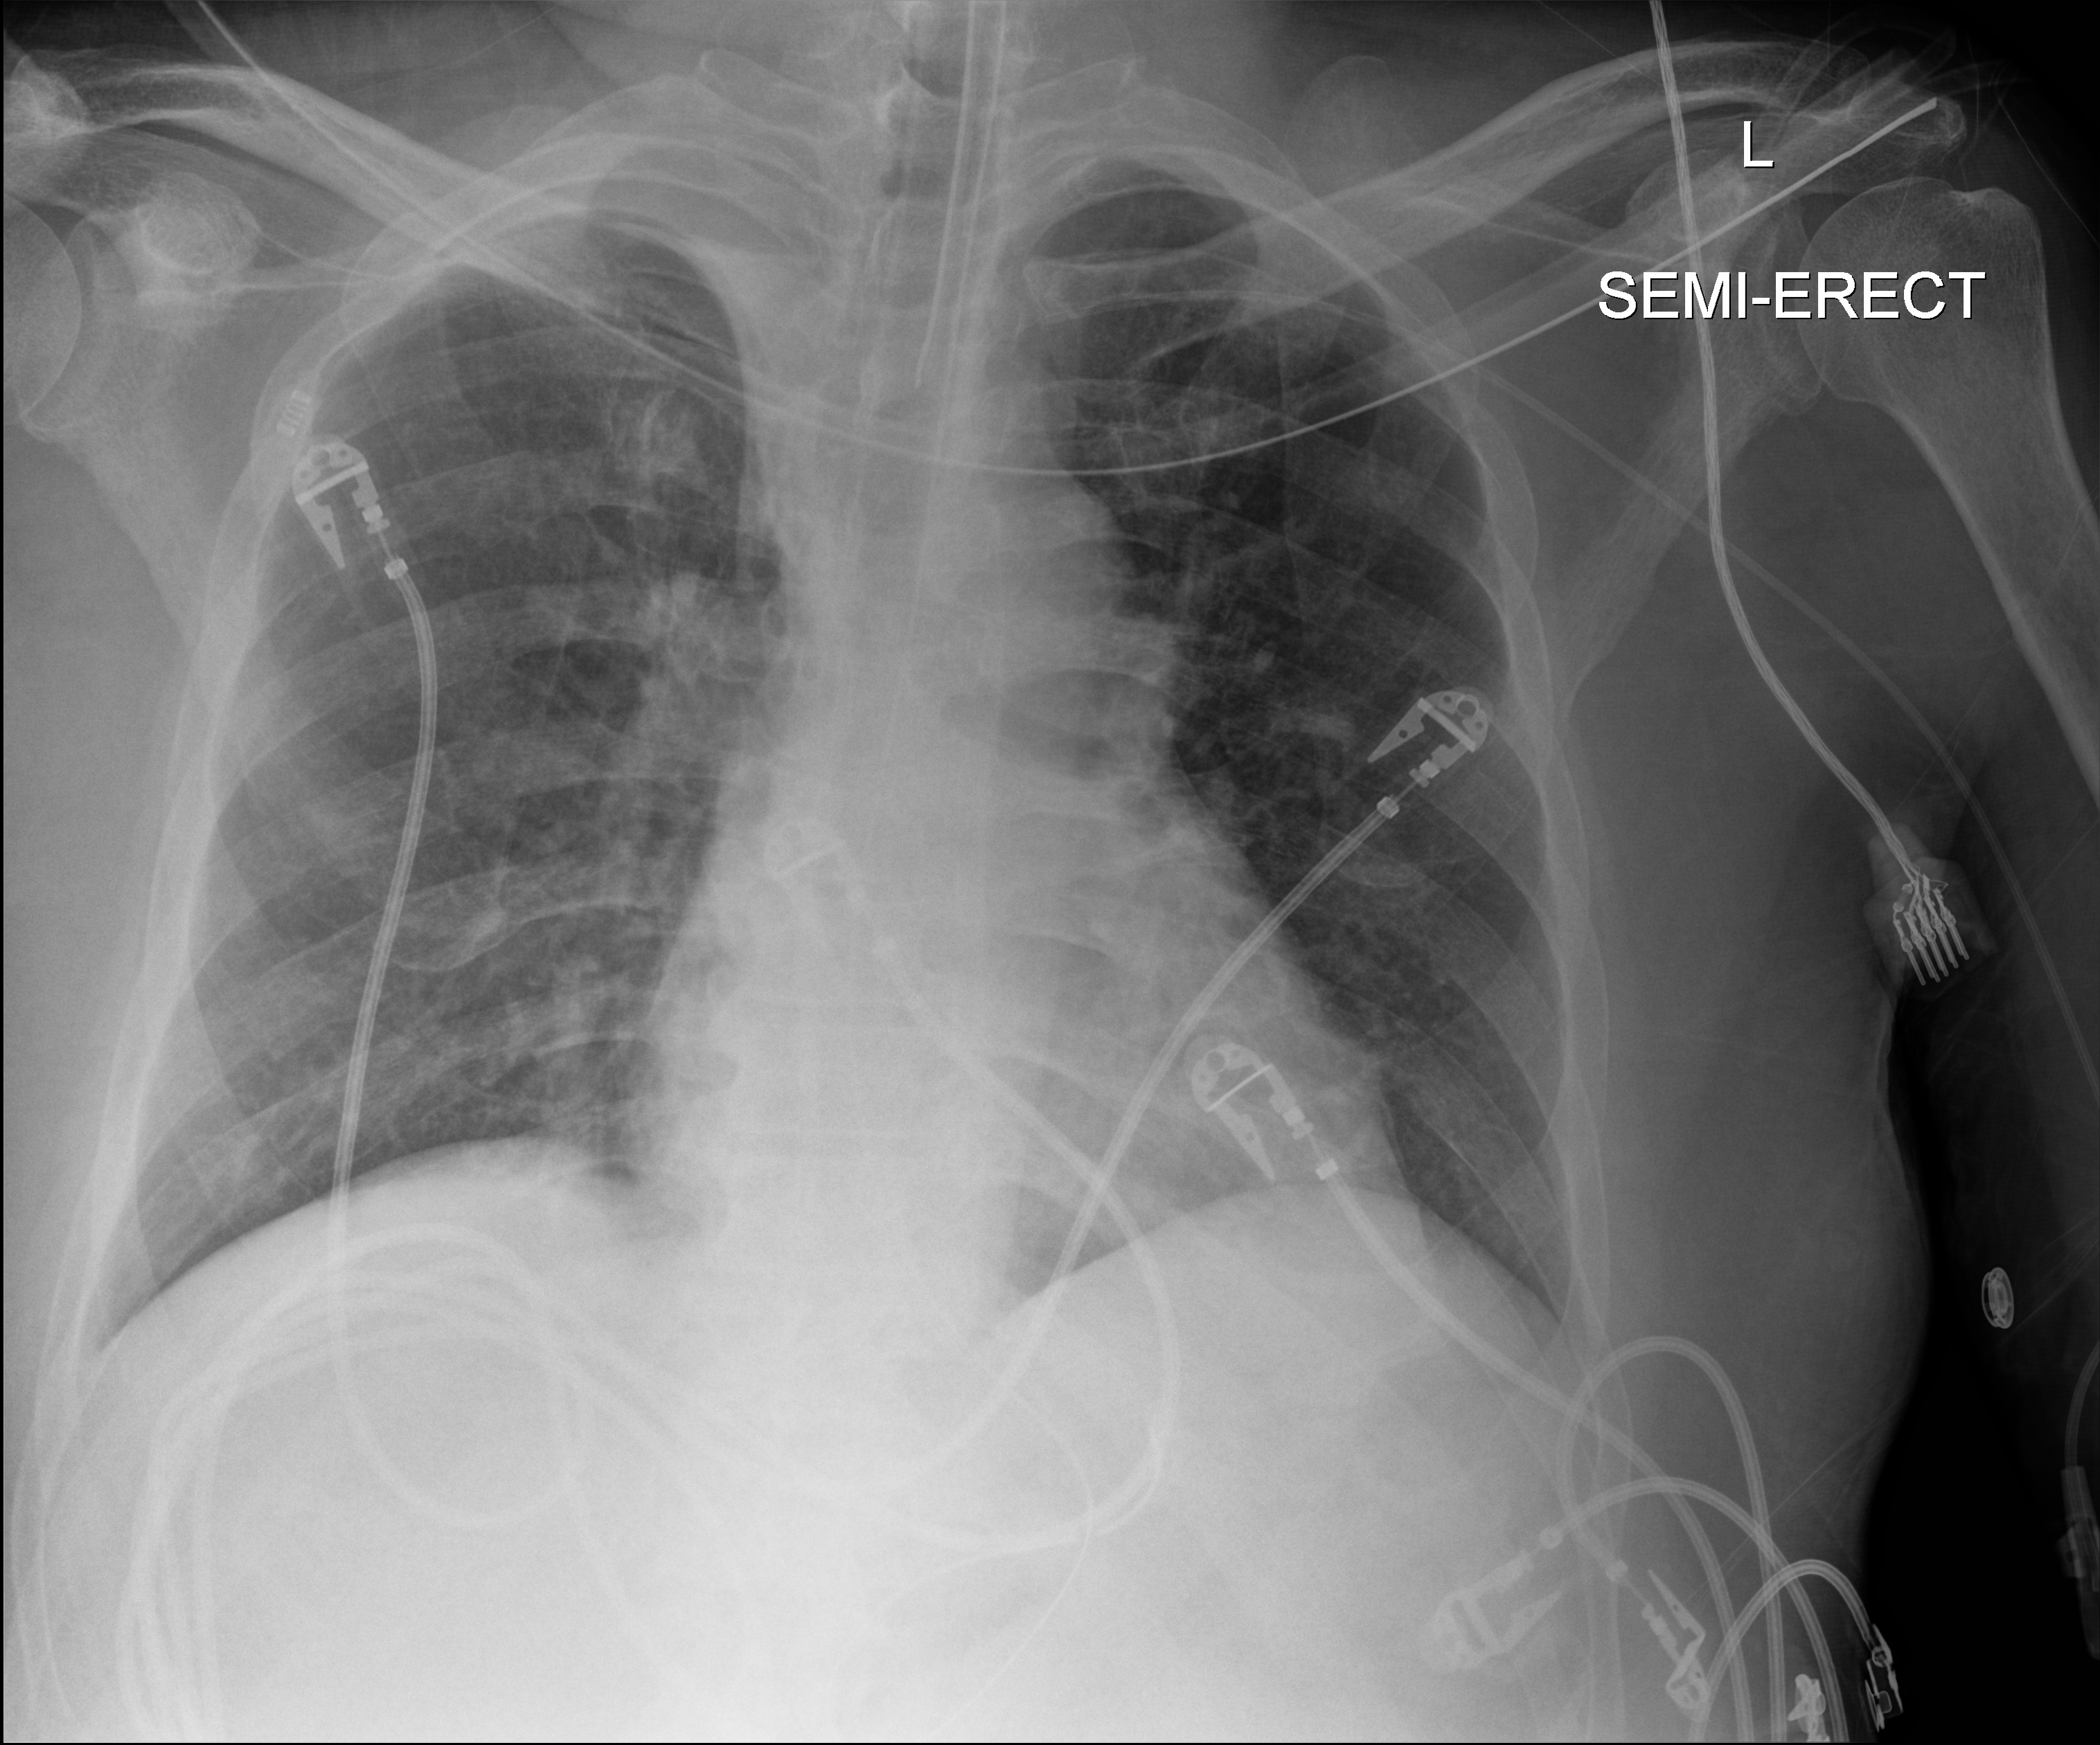
Chest X-ray (portable), anteroposterior (AP) projection. Patient hospitalised with COVID-19, aged 18–59 years.
Admission-level facts for this patient (not findings on this image; timing relative to this image not recorded):
- diabetes (admission record): yes
- mechanically ventilated during this hospital stay: yes